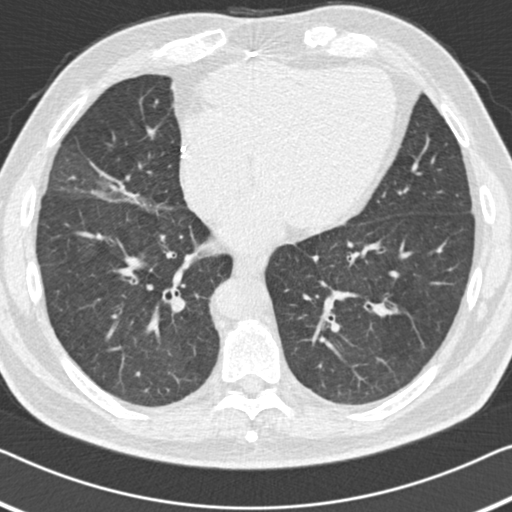
Low-dose screening chest CT, one axial slice. Position 60 of 155 along the scan axis. Reconstruction kernel B30f. 120 kVp. Lung window (W 1500 / L -600 HU). 2 mm slice thickness. 512 × 512 image matrix, field of view 332 × 332 mm.
Outlined on this slice (outlined manually by an expert reader):
- lesion 1 (tumor): bounding box (x1, y1, x2, y2) in pixels: (210, 310, 212, 315)